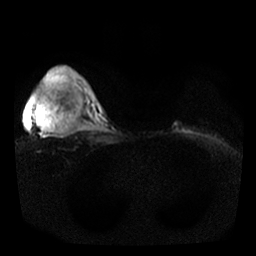
Breast MRI, one axial slice; slice 23 of 25 in the series (ordered by position); diffusion-weighted series; image 2 of 4 stored at this slice position (different b-values; order by instance number); 1.5 T; 4 mm slice thickness; 256 × 256 image matrix, field of view 350 × 350 mm. Female patient.
Structures marked on this image (manually delineated by an expert):
- tumour on diffusion-weighted imaging: bounding box (x1, y1, x2, y2) in pixels: (38, 68, 65, 129)